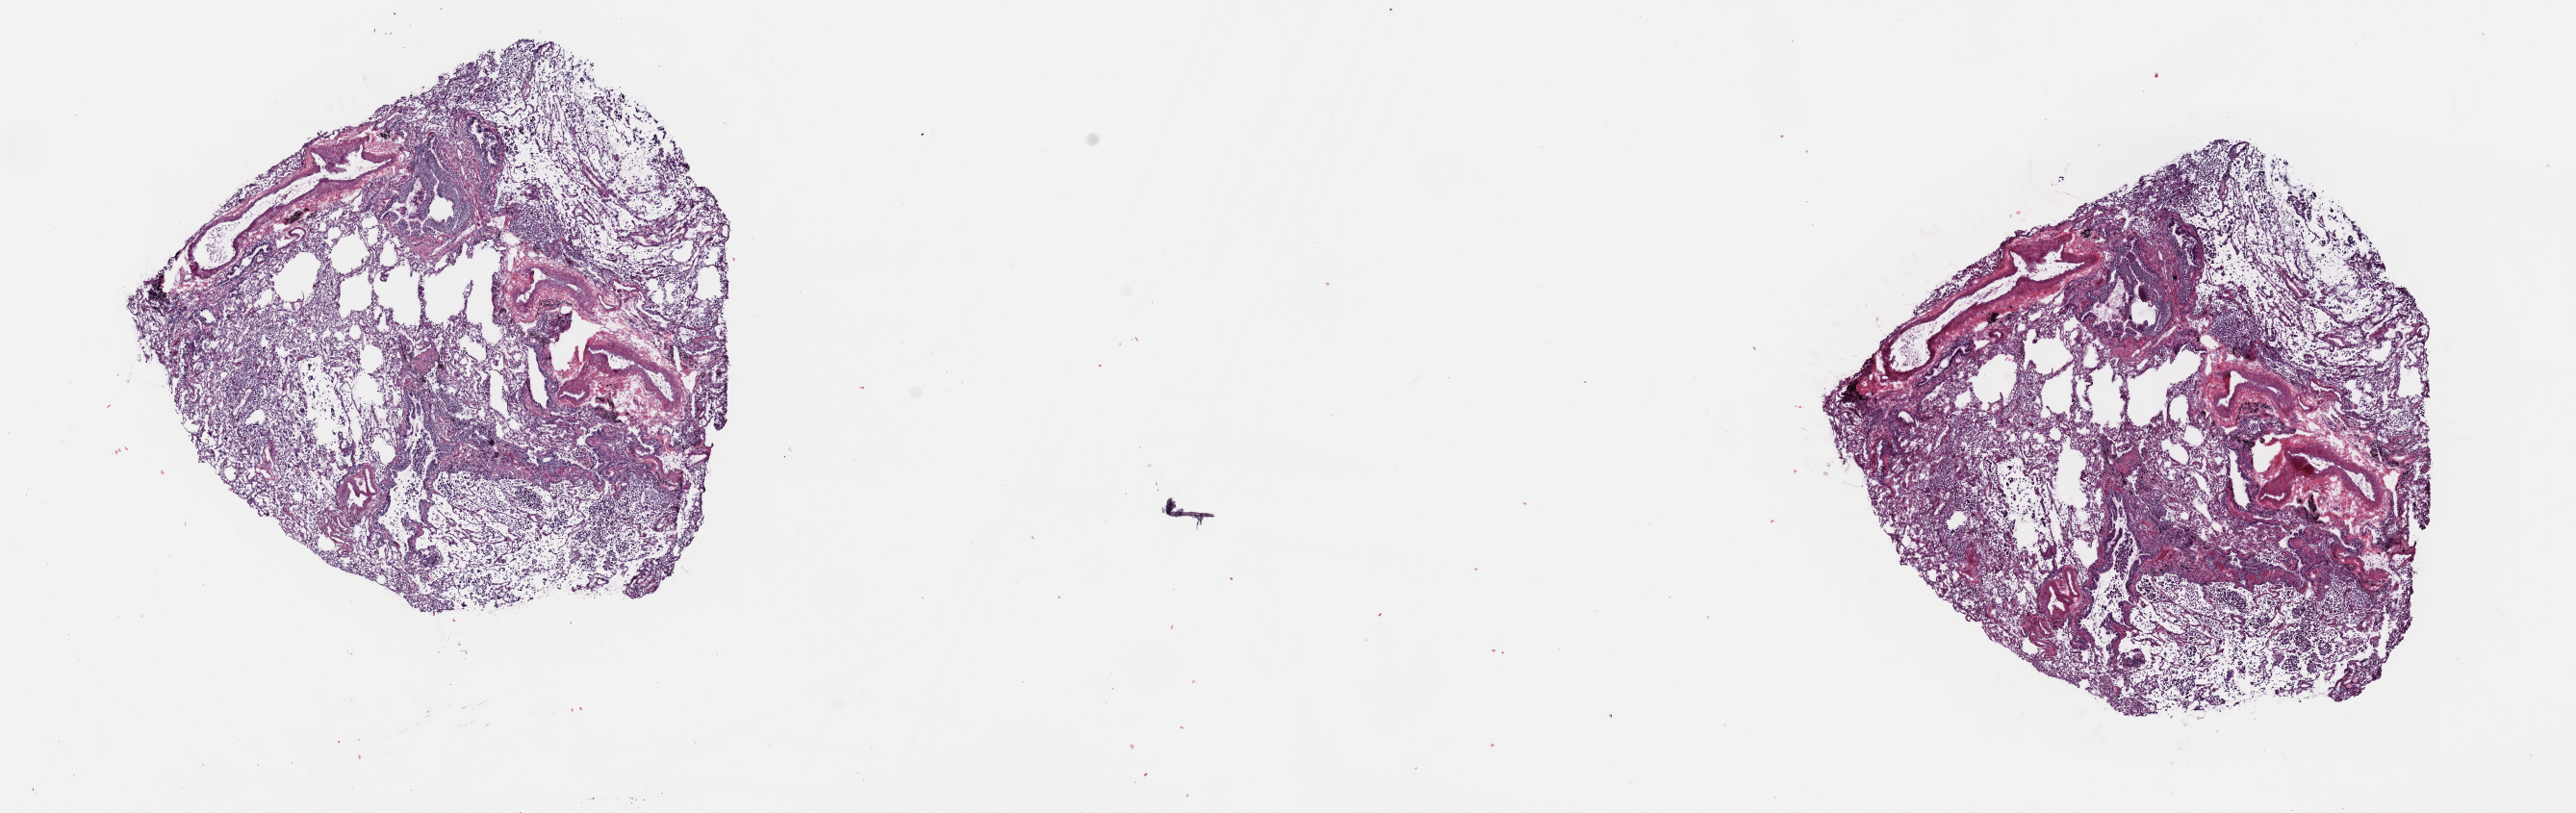
Digitized H&E tissue section (whole slide), a low-resolution overview of the entire scanned area, about 21.1 x 6.7 mm (slide scanned at 40x), frozen section from the top of the tissue portion, lung, primary tumour sample. Male, age 78 years at initial diagnosis. Composition of this section per pathologist review: tumour cells 90%, tumour nuclei 75%, normal cells 10%, stromal cells 0%, necrosis 0%. Inflammatory infiltration, as recorded: lymphocyte infiltration 2%, monocyte infiltration 3%, neutrophil infiltration 0%.
AJCC pathologic stage: IIA. Histologic diagnosis: Adenocarcinoma, NOS (lower lobe, lung). Laterality: left.